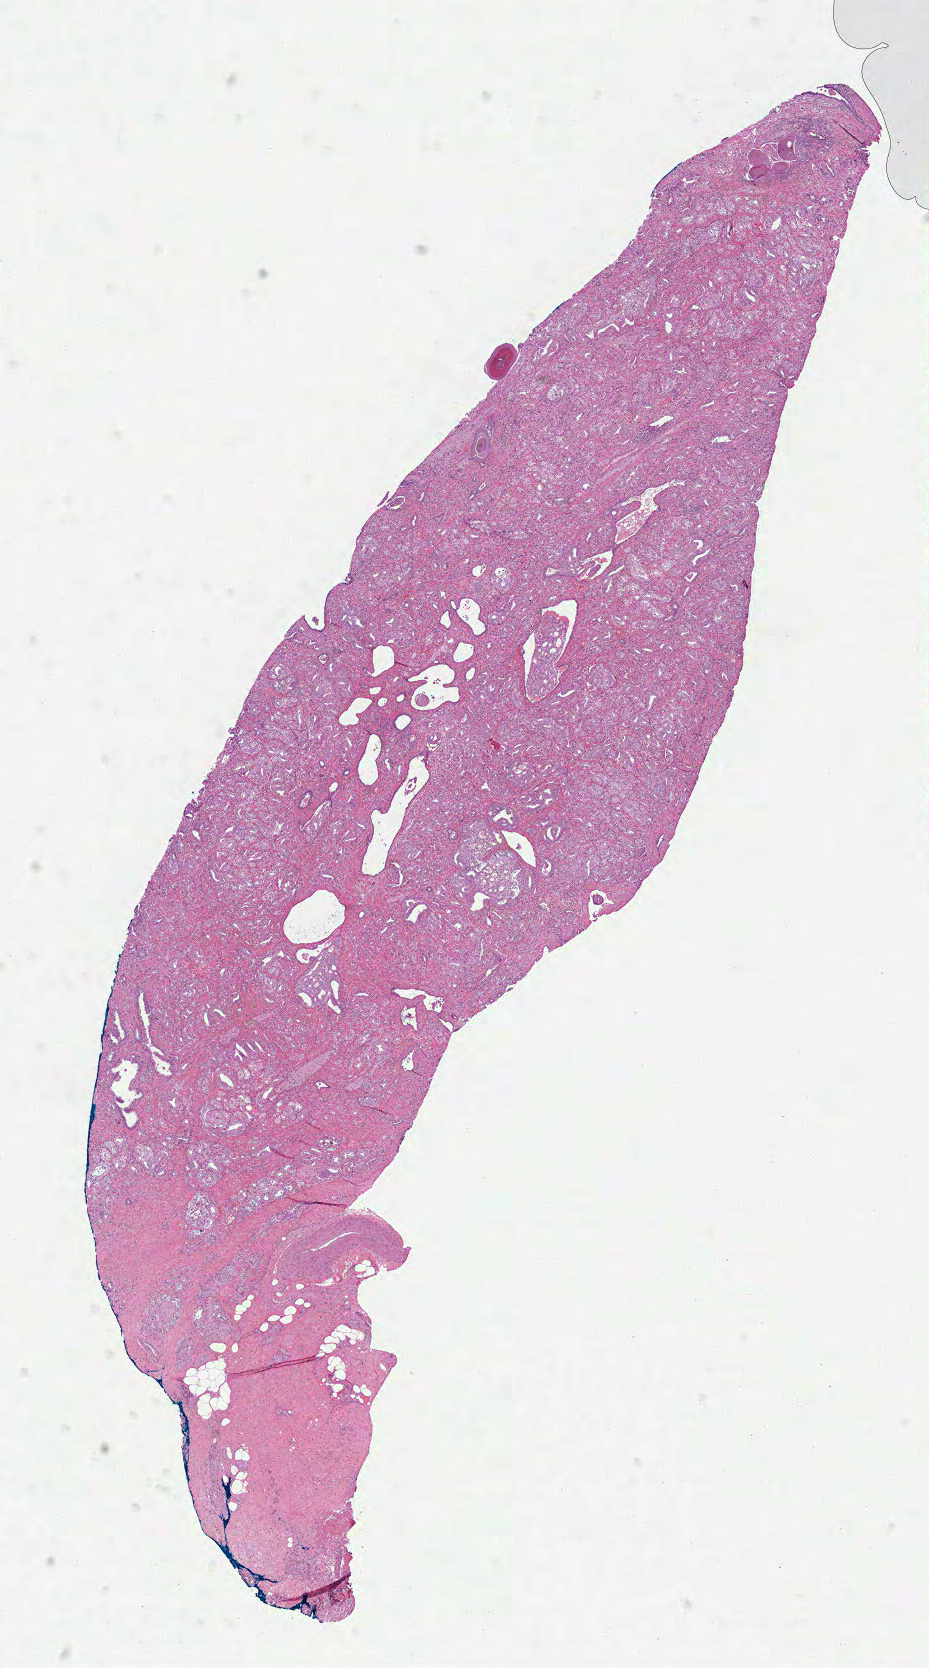
Hematoxylin and eosin (H&E) stained whole-slide image, low-resolution overview of the scanned area, about 7.5 x 13.5 mm (from a 40x scan). Formalin-fixed paraffin-embedded (FFPE) diagnostic section. Primary tumour sample from the prostate. Male, age 53 years at initial diagnosis. Gleason score: 7 (3+4).
Lymph nodes positive (case pathology): 0 of 3 examined. Laterality: bilateral. Diagnosis: Acinar cell carcinoma (prostate gland).